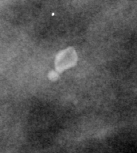
Cropped region of a digitized screen-film mammogram centred on a radiologist-marked abnormality; right breast; MLO view; BI-RADS breast density category 3 (scale 1–4).
- Marked abnormality: calcifications, morphology round and regular / lucent center; BI-RADS assessment category 2; subtlety rating 4 on a 1 (subtle) to 5 (obvious) scale; benign; no additional work-up was recommended (benign without callback).